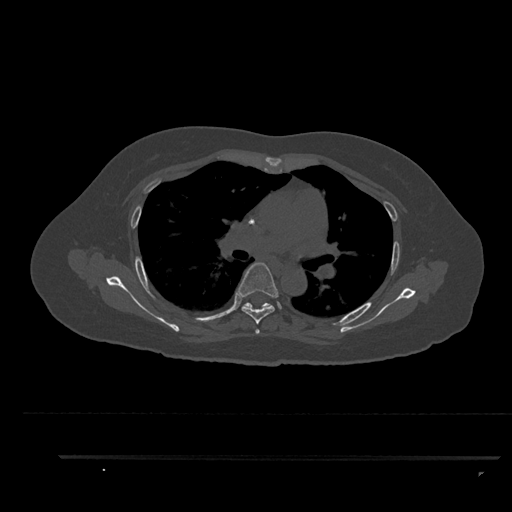
CT including the spine, one axial slice. Slice 593 of 797 in the series (ordered by position). Reconstruction kernel Br40s/3. 120 kVp. Bone window (W 1800 / L 400 HU). 512 × 512 image matrix. Female patient, age 44 years. Case-level facts recorded for this patient, not image findings: primary cancer: renal.
Structures marked on this image (semi-automatically segmented with operator editing):
- T4 vertebra: box from (x=255, y=329) to (x=260, y=334) px
- T5 vertebra: (x=238, y=262)–(x=279, y=324)
- T6 vertebra: (x=242, y=302)–(x=273, y=309)